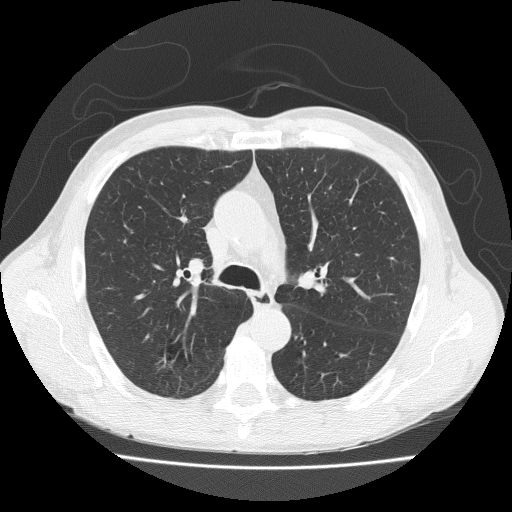
Low-dose screening chest CT, axial slice. Baseline screening round. Lung window (W 1500 / L -600 HU). 2 mm slice thickness. Lung (sharp) reconstruction kernel (FC51). Slice 70 of 203 in the series. Male, age 73 years at enrolment. Current smoker at enrolment.
Expert reader's lesion annotation, bounding box (x1, y1, x2, y2) in pixels: (145, 337, 197, 384). No non-calcified nodule or mass ≥4 mm was recorded by the screening reader at this exam. Official screen result: negative screen, no significant abnormalities.